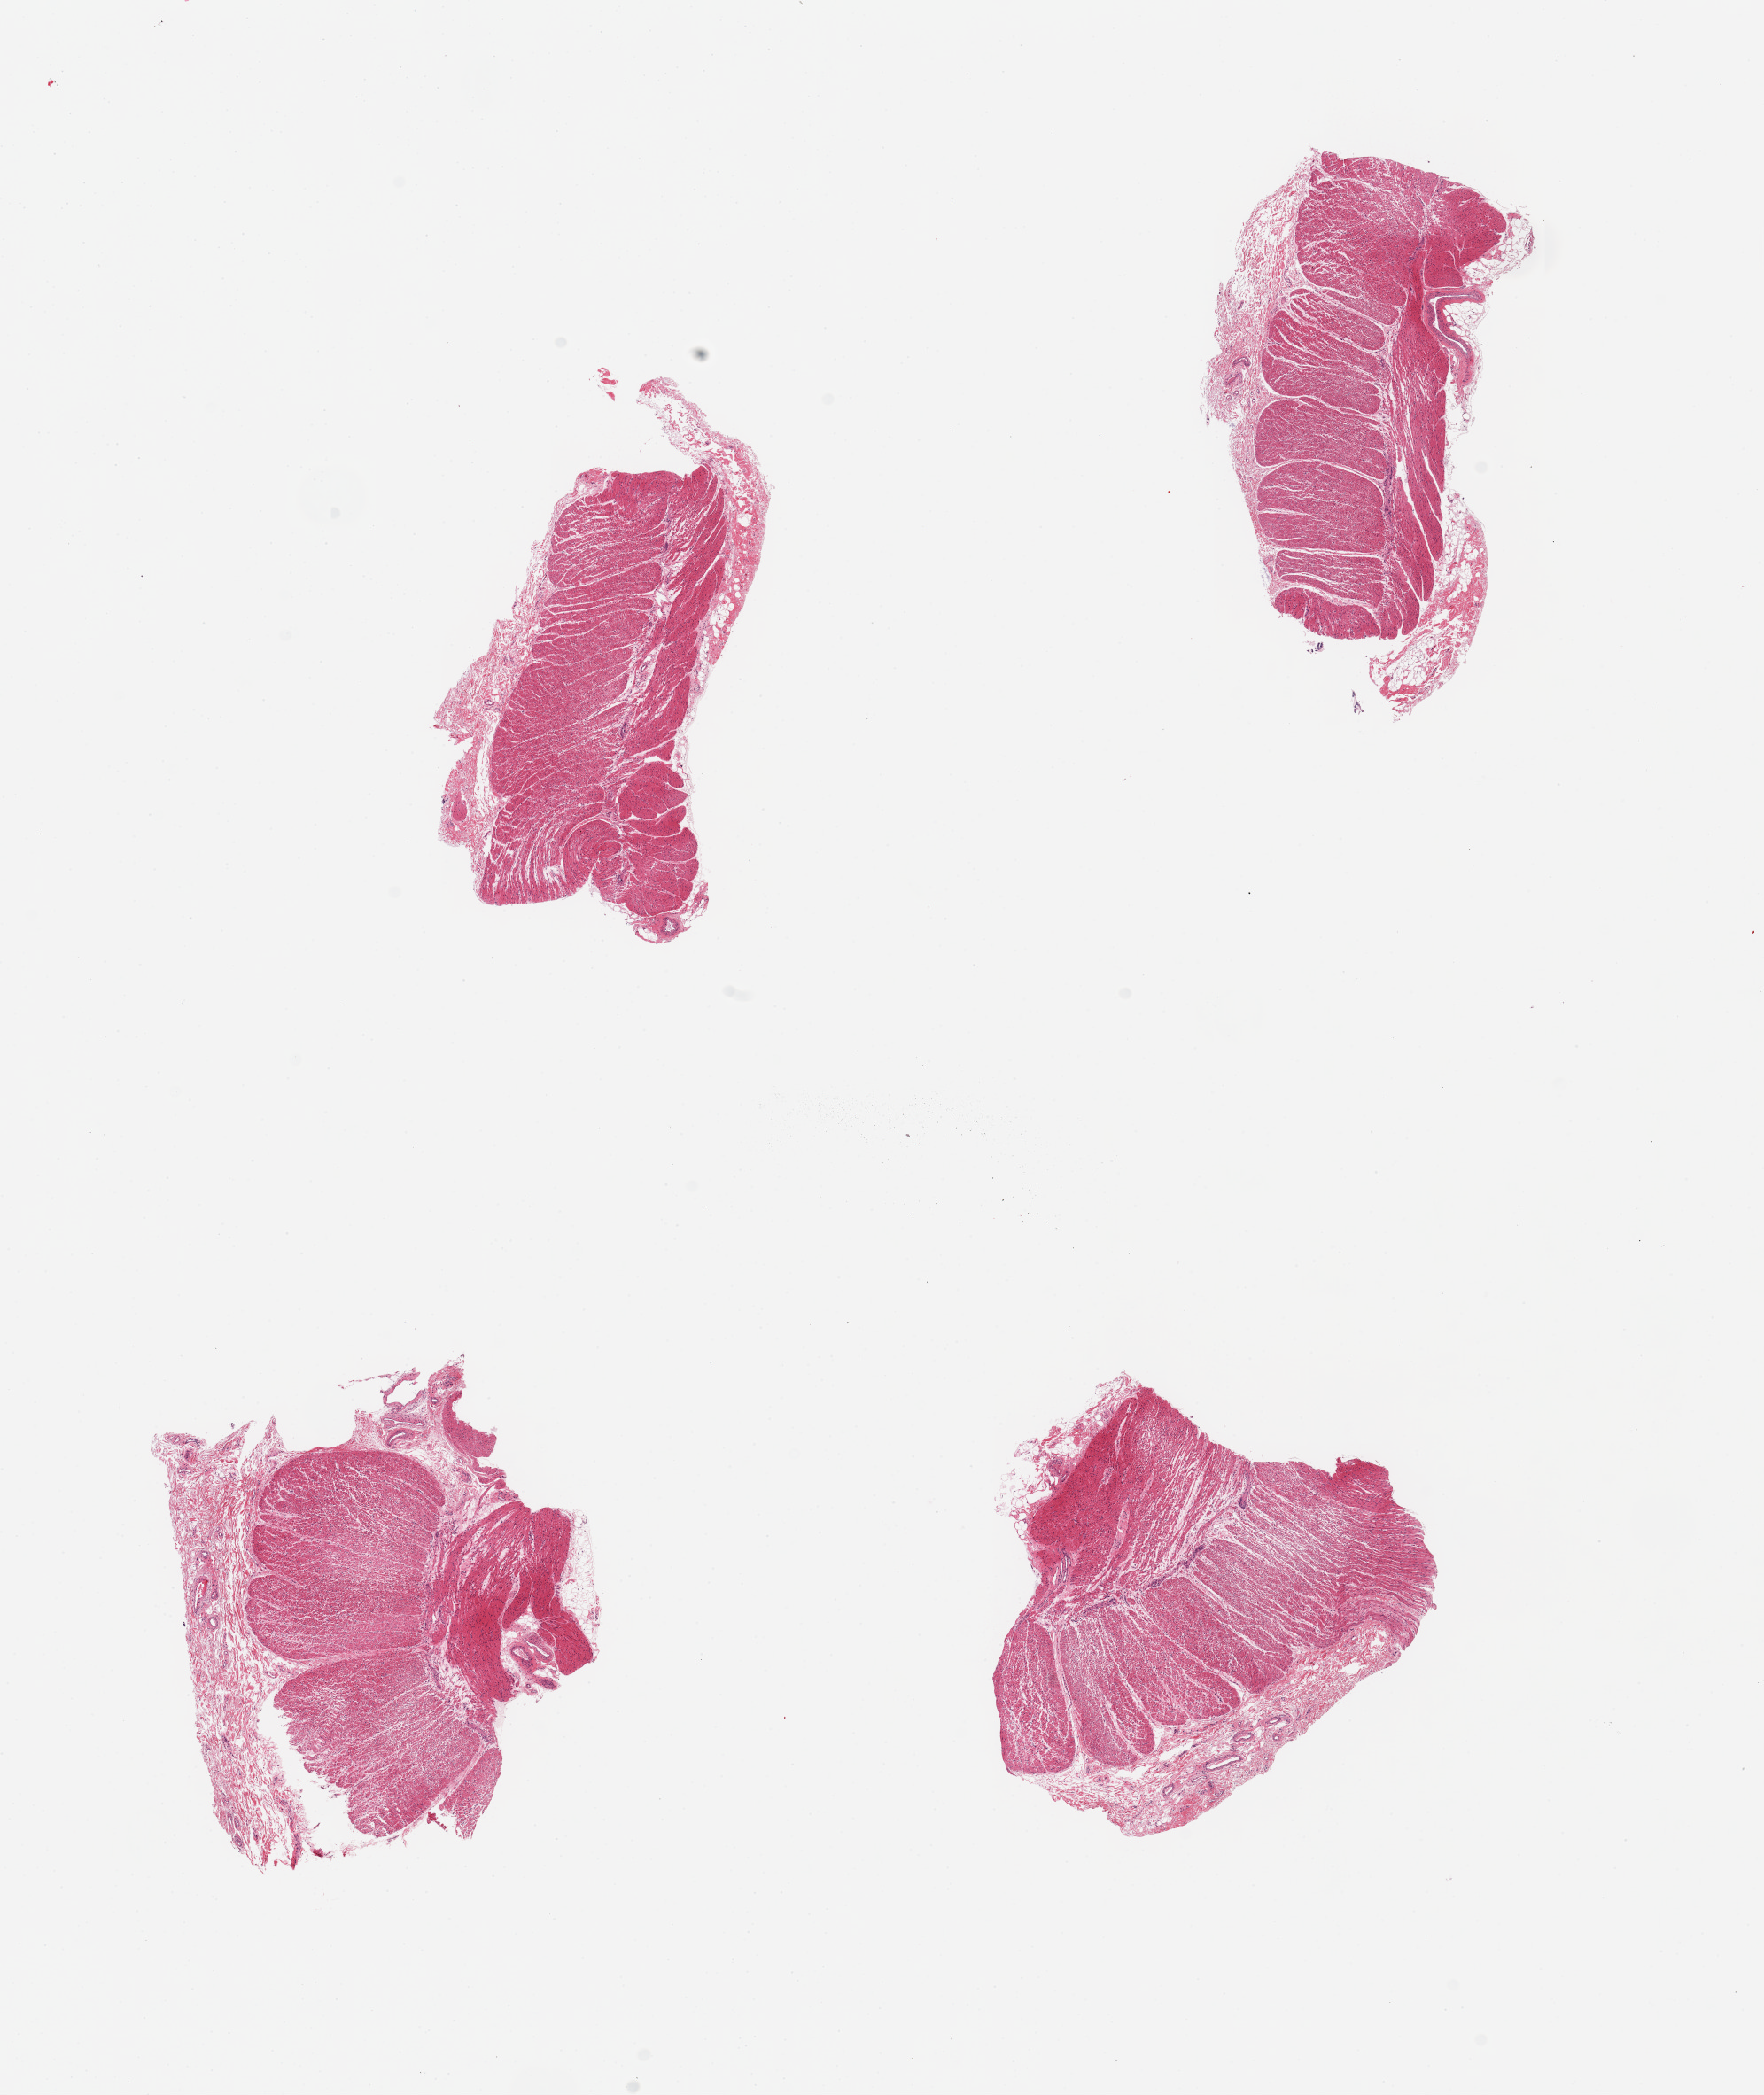
Whole-slide image, H&E stain — whole scanned area (about 15.8 x 18.7 mm, acquisition: 20x scan) shown as a low-resolution overview. PAXgene-fixed, paraffin-embedded tissue. Section of sigmoid colon (target tissue). Donor tissue sample.
Reviewer comment on this tissue sample: 4 pieces; muscularis and submucosa.